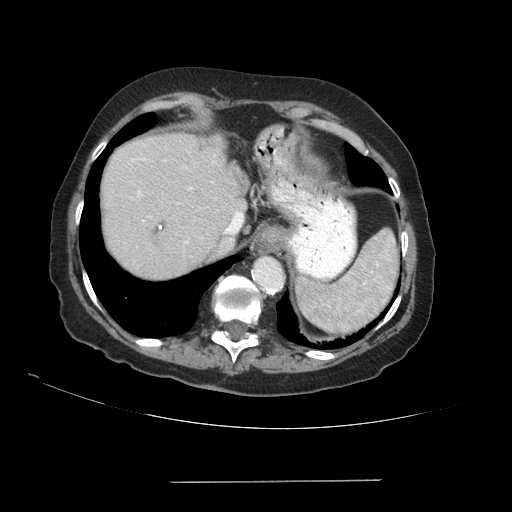
Contrast-enhanced abdominal CT (liver protocol), one axial slice. Position 73 of 89 along the scan axis. 140 kVp. Soft-tissue window (W 400 / L 40 HU). 2.5 mm slice thickness. 512 × 512 image matrix, field of view 400 × 400 mm. Case-level facts recorded for this patient, not image findings: diagnosis: hepatocellular carcinoma (patient treated with transarterial chemoembolisation; whether this scan precedes or follows treatment is not stated here); TNM stage (as recorded): Stage-IVA; Child-Pugh class: A; tumour differentiation: poorly differentiated; tumour nodularity: uninodular.
Outlined on this slice (semi-automatic segmentation, software-assisted and operator-edited):
- abdominal aorta: box from (x=254, y=258) to (x=281, y=287) px
- liver parenchyma outside the tumour (the mass and vessels are separate outlines, so this box may not span the whole liver): (x=102, y=132)–(x=246, y=278)
- liver vessels: (x=132, y=159)–(x=240, y=243)